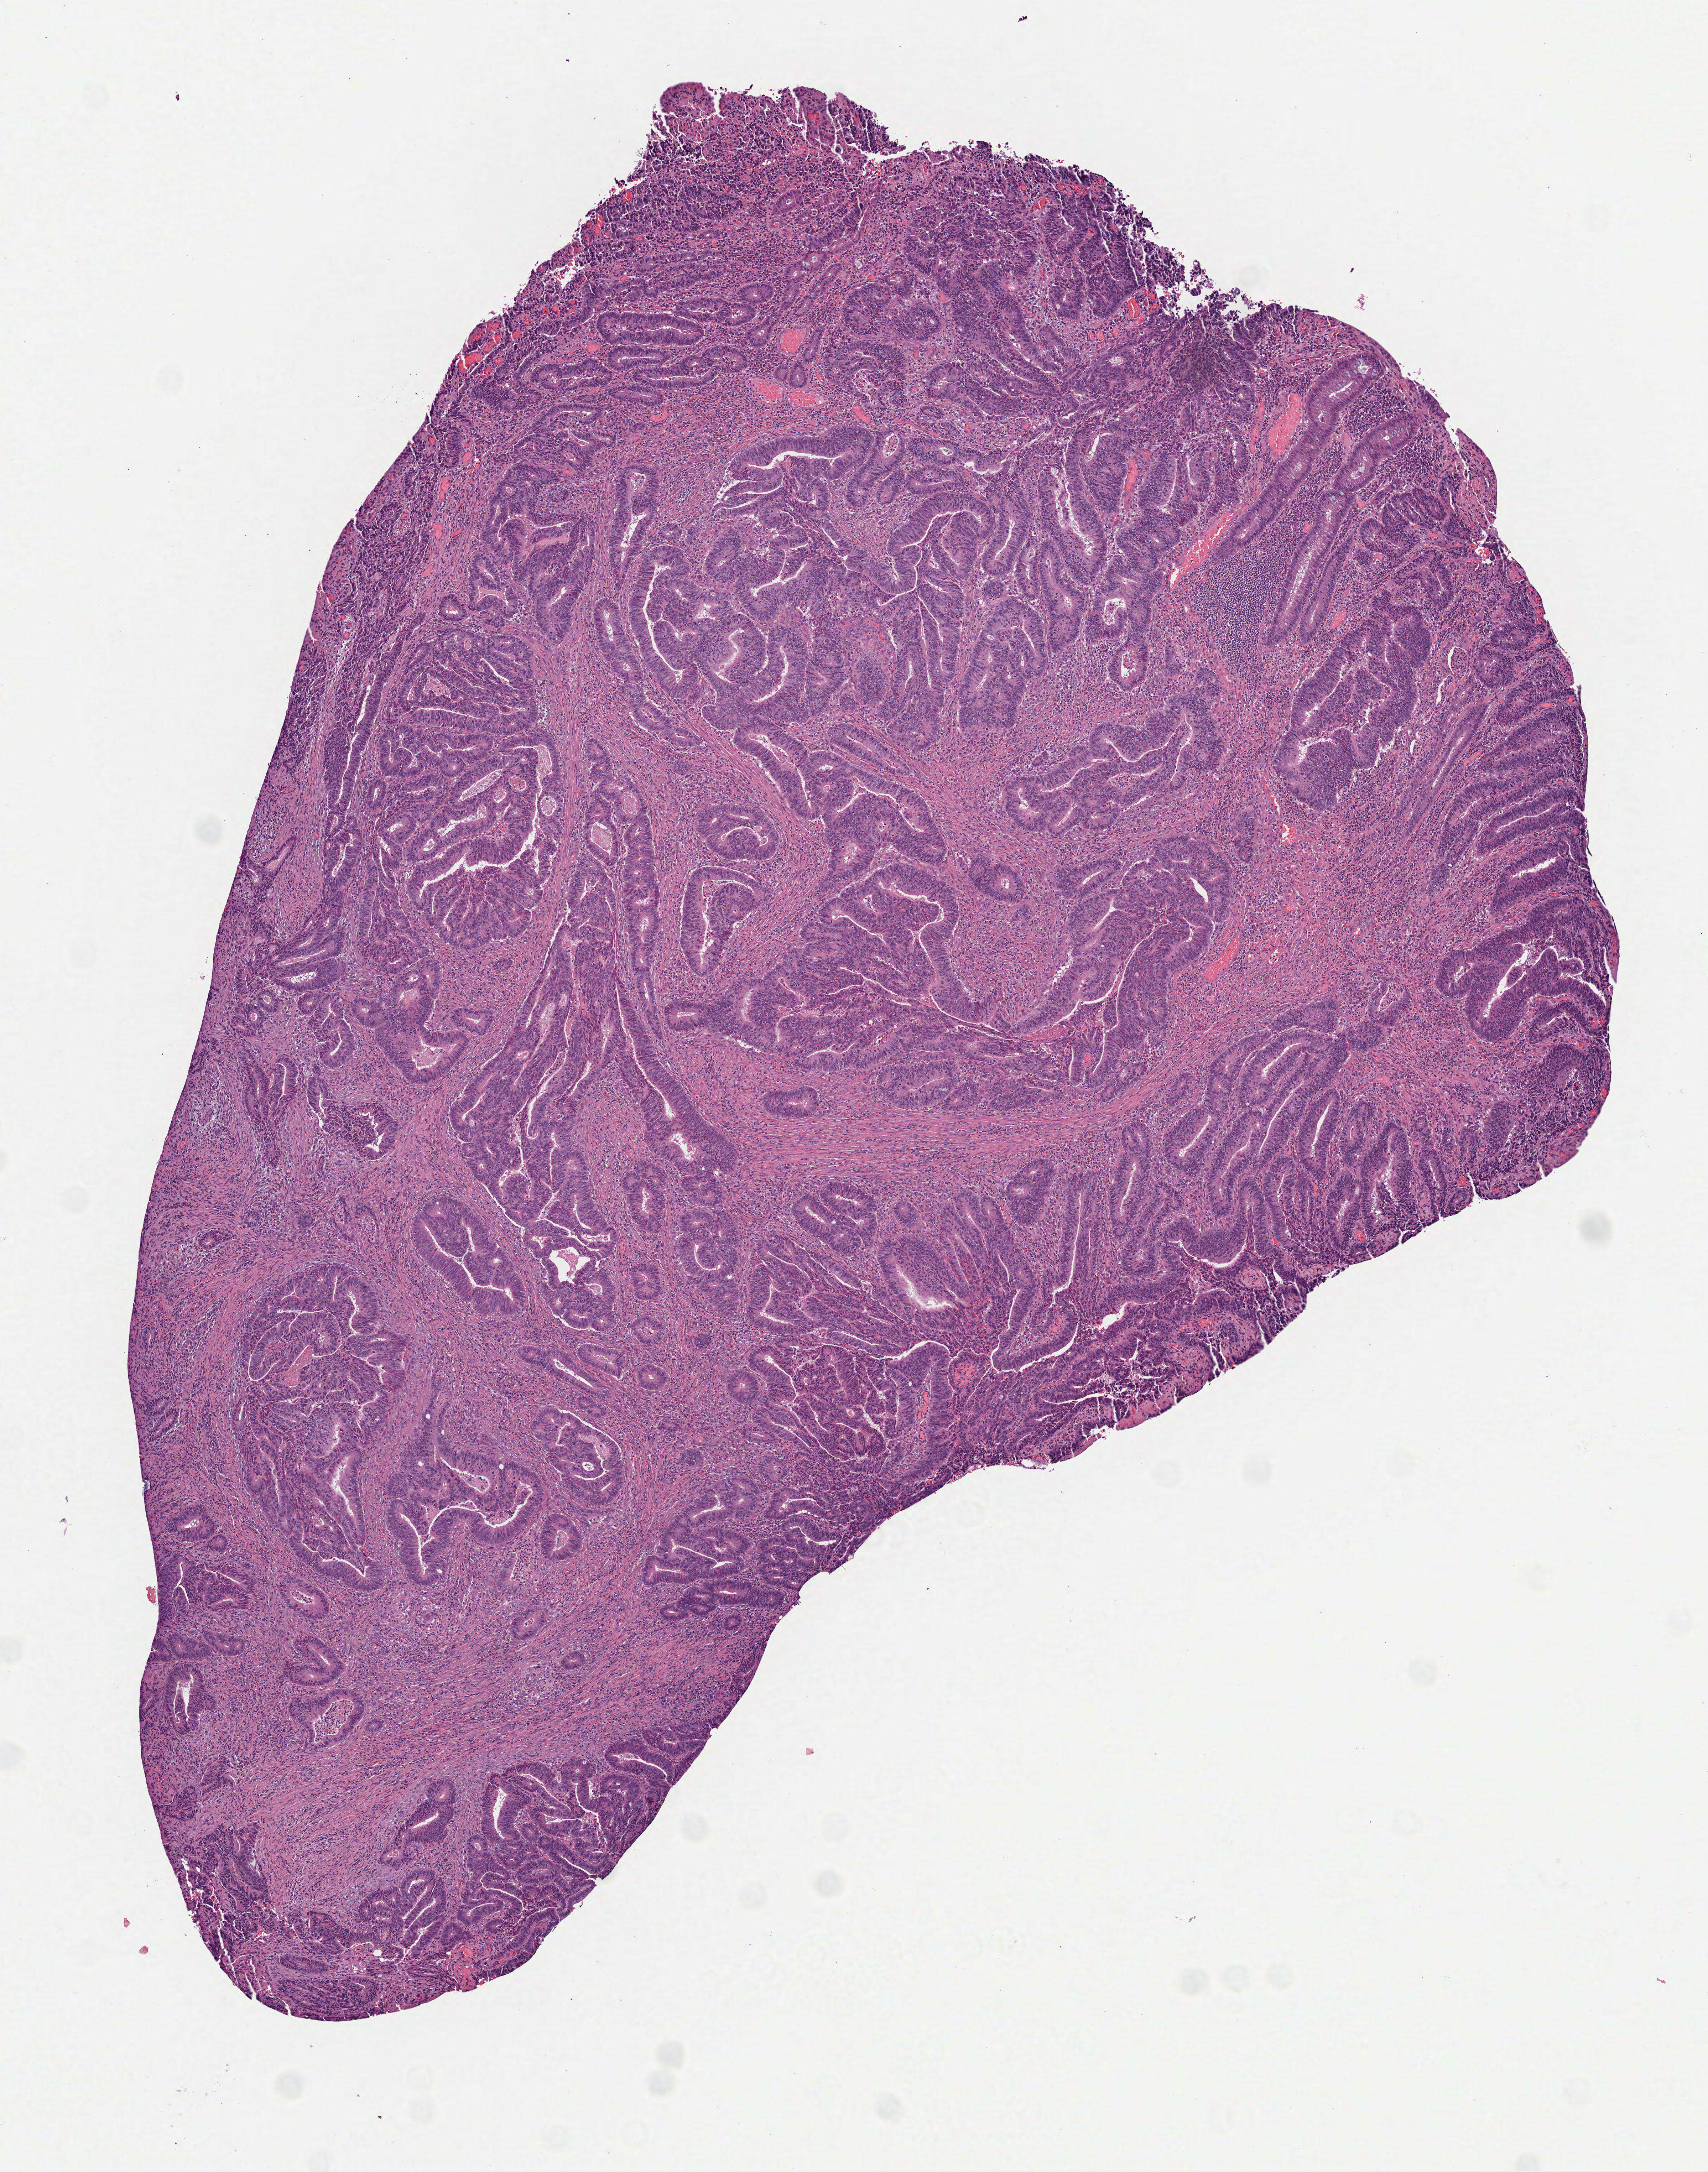
H&E whole-slide image — a low-resolution overview of the entire scanned area, about 4.8 x 6.1 mm (acquisition: 40x scan). Formalin-fixed paraffin-embedded (FFPE) diagnostic section. Primary tumour sample from the rectum. Female patient; age at initial diagnosis 79 years.
Lymph nodes positive (case pathology): 0 of 21 examined. Histologic diagnosis: Adenocarcinoma, NOS (rectosigmoid junction).